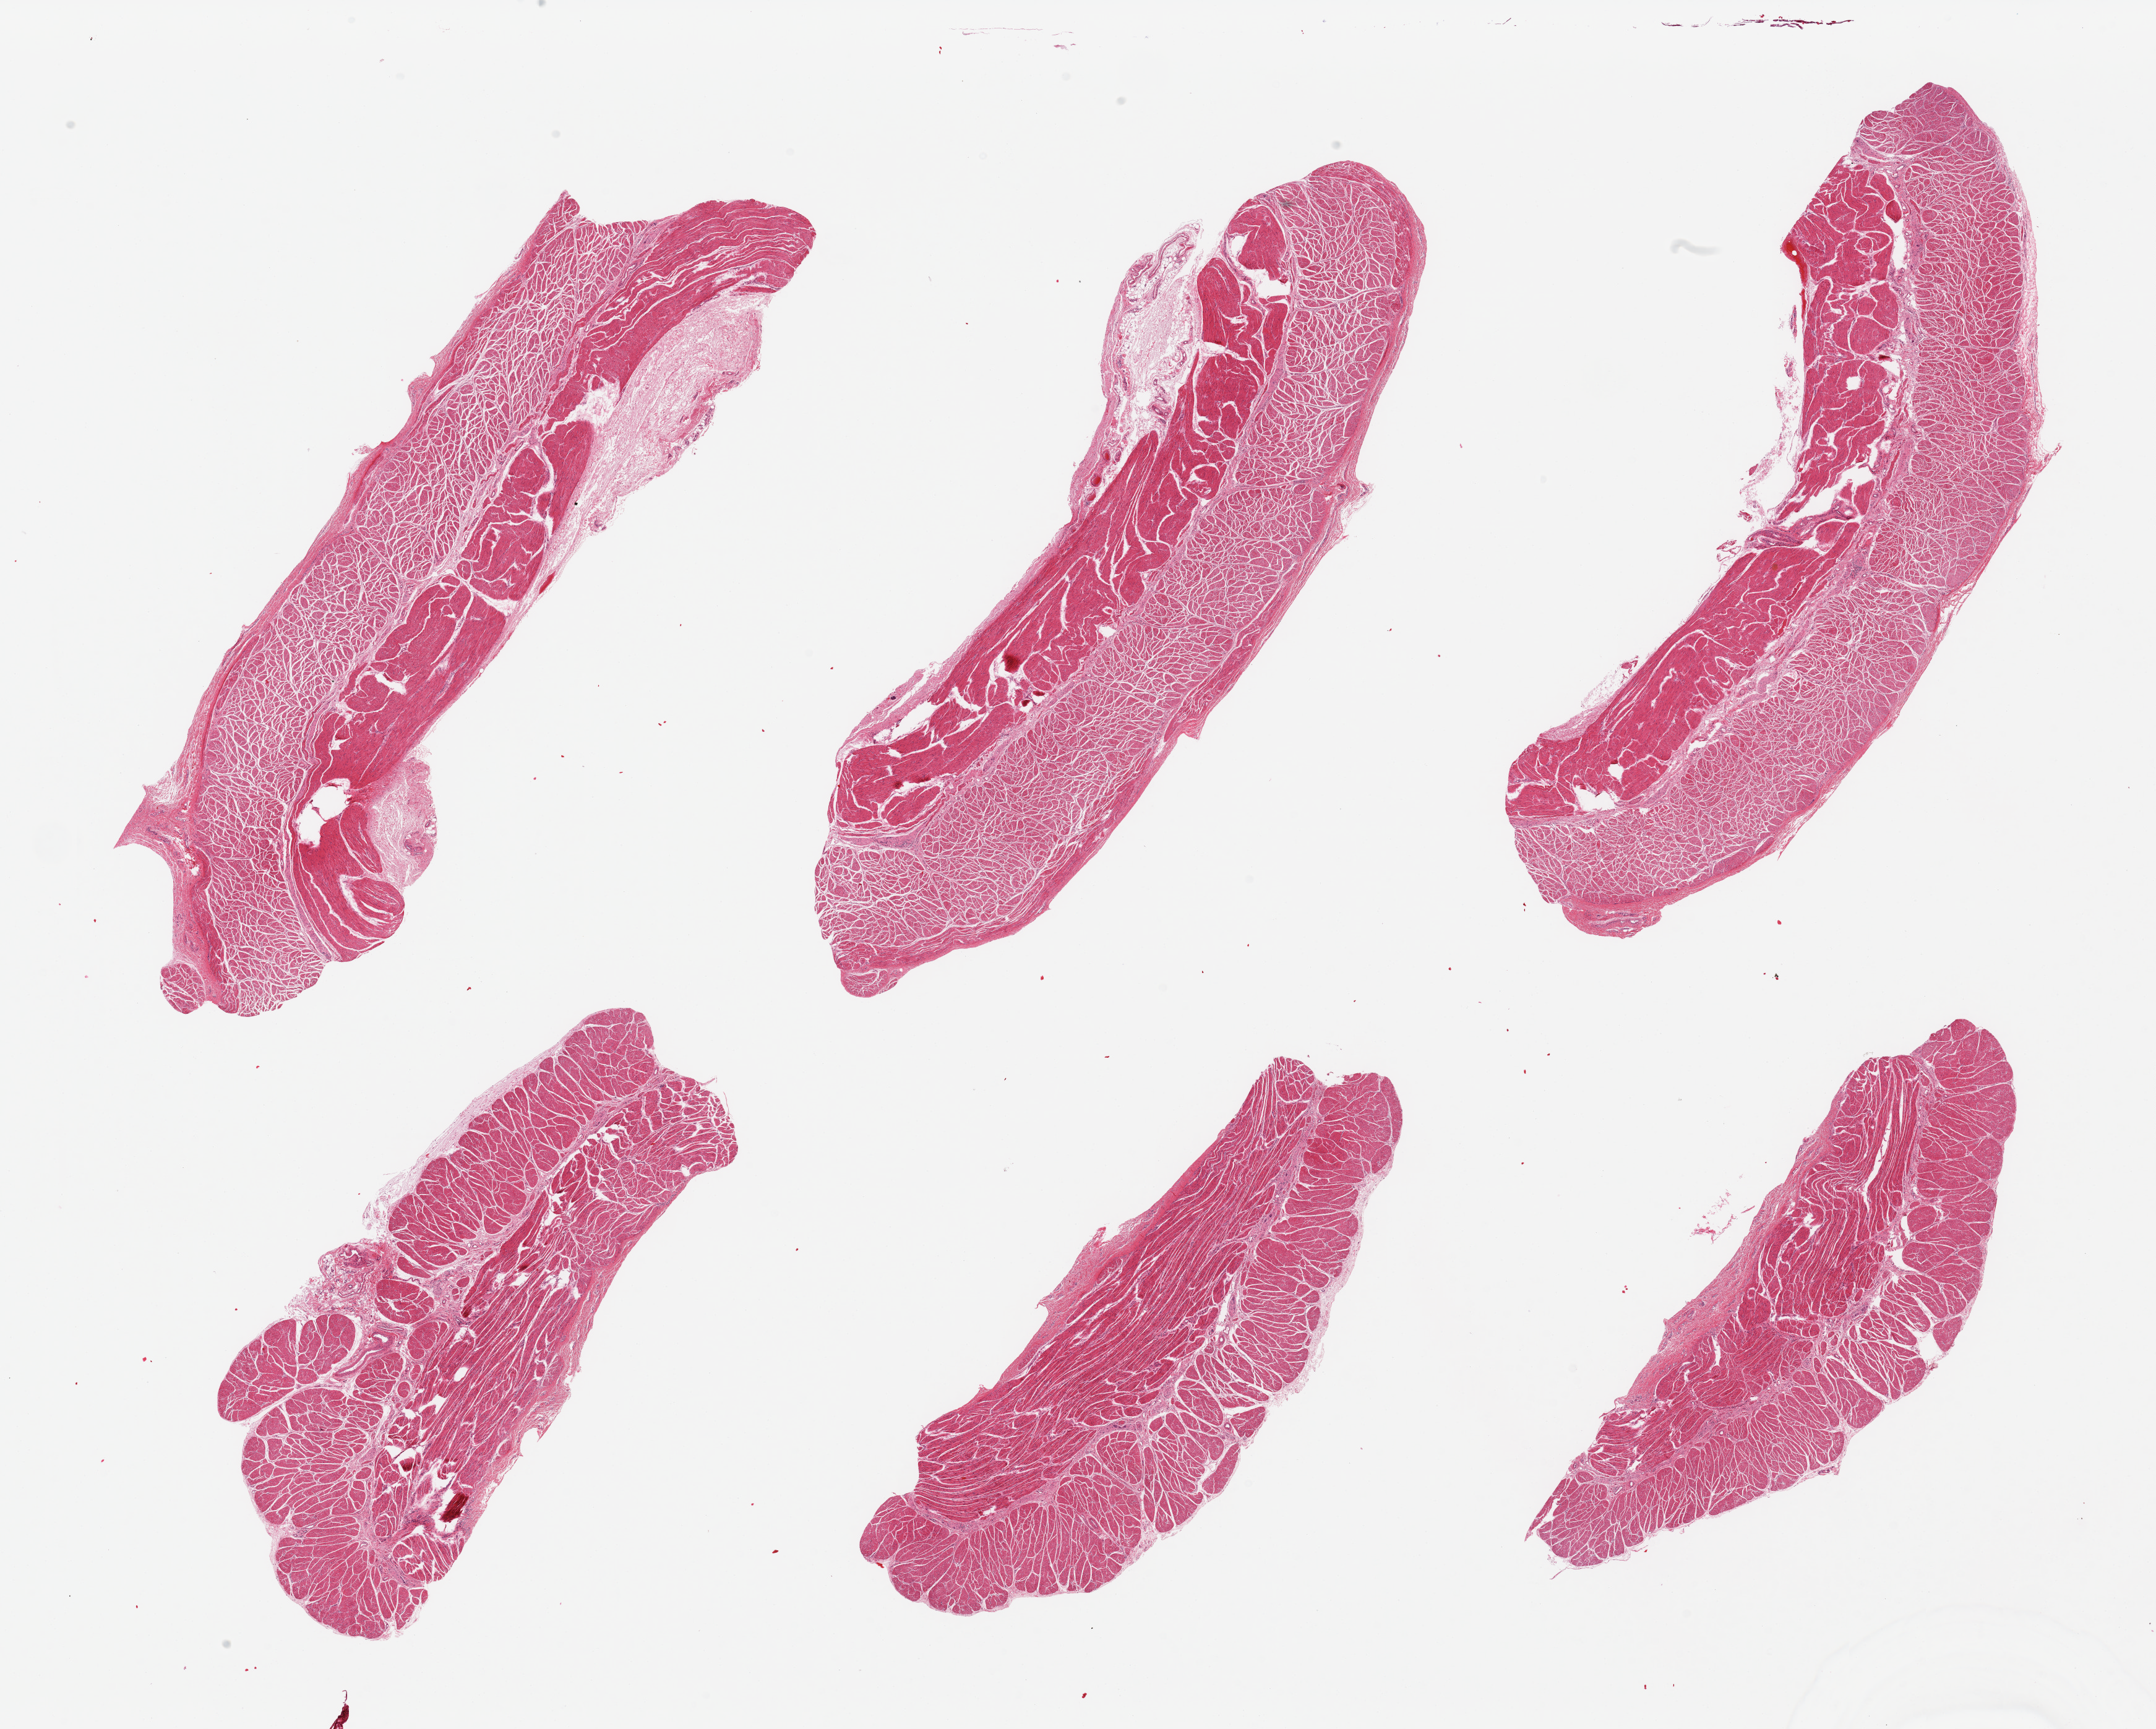
Digitized H&E-stained section — shown as a low-resolution overview of the whole scanned area (about 27.6 x 22.1 mm). PAXgene-fixed, paraffin-embedded tissue. Sampled site (target tissue): esophageal muscle. Tissue donor sample. Donor sex: male.
Pathologist's review note for this sample: 6 pieces; target muscularis.